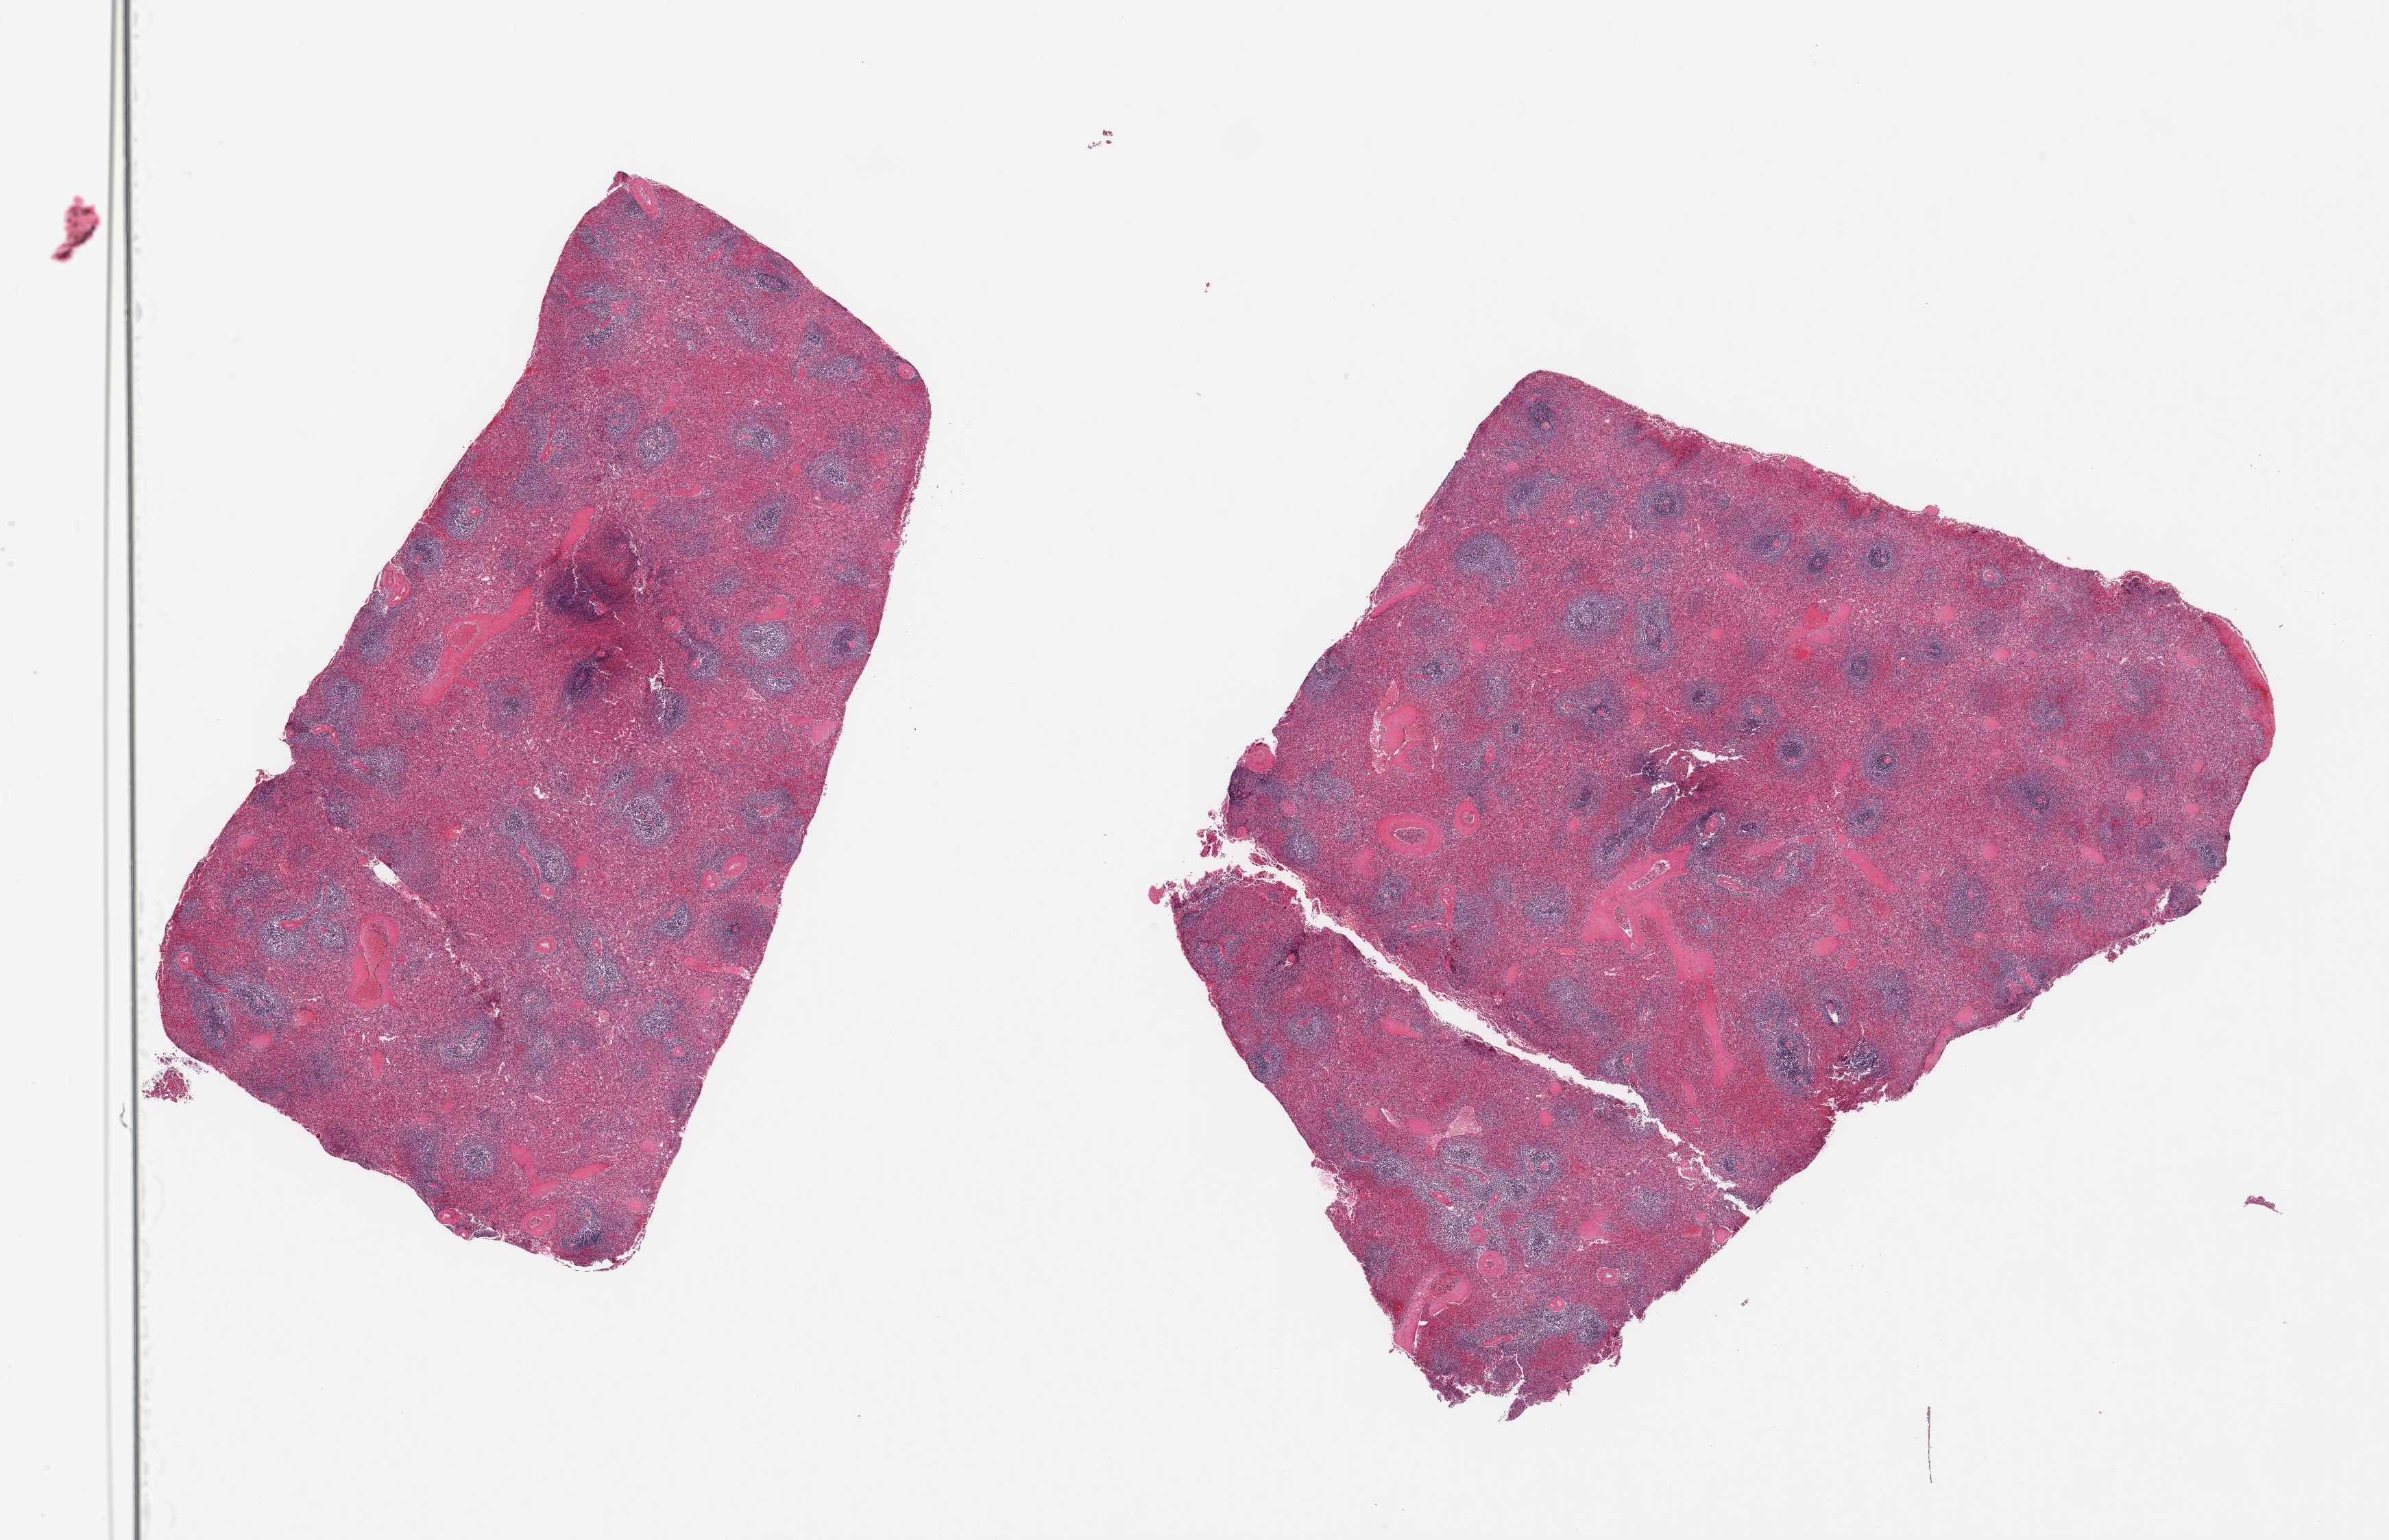
Digitized haematoxylin and eosin-stained section — low-resolution overview of the scanned area, about 27.6 x 17.8 mm, PAXgene-fixed paraffin-embedded (PFPE) section, section of spleen (target tissue), donor tissue sample.
Reviewer comment on this tissue sample: 2 pieces; mild congestion.